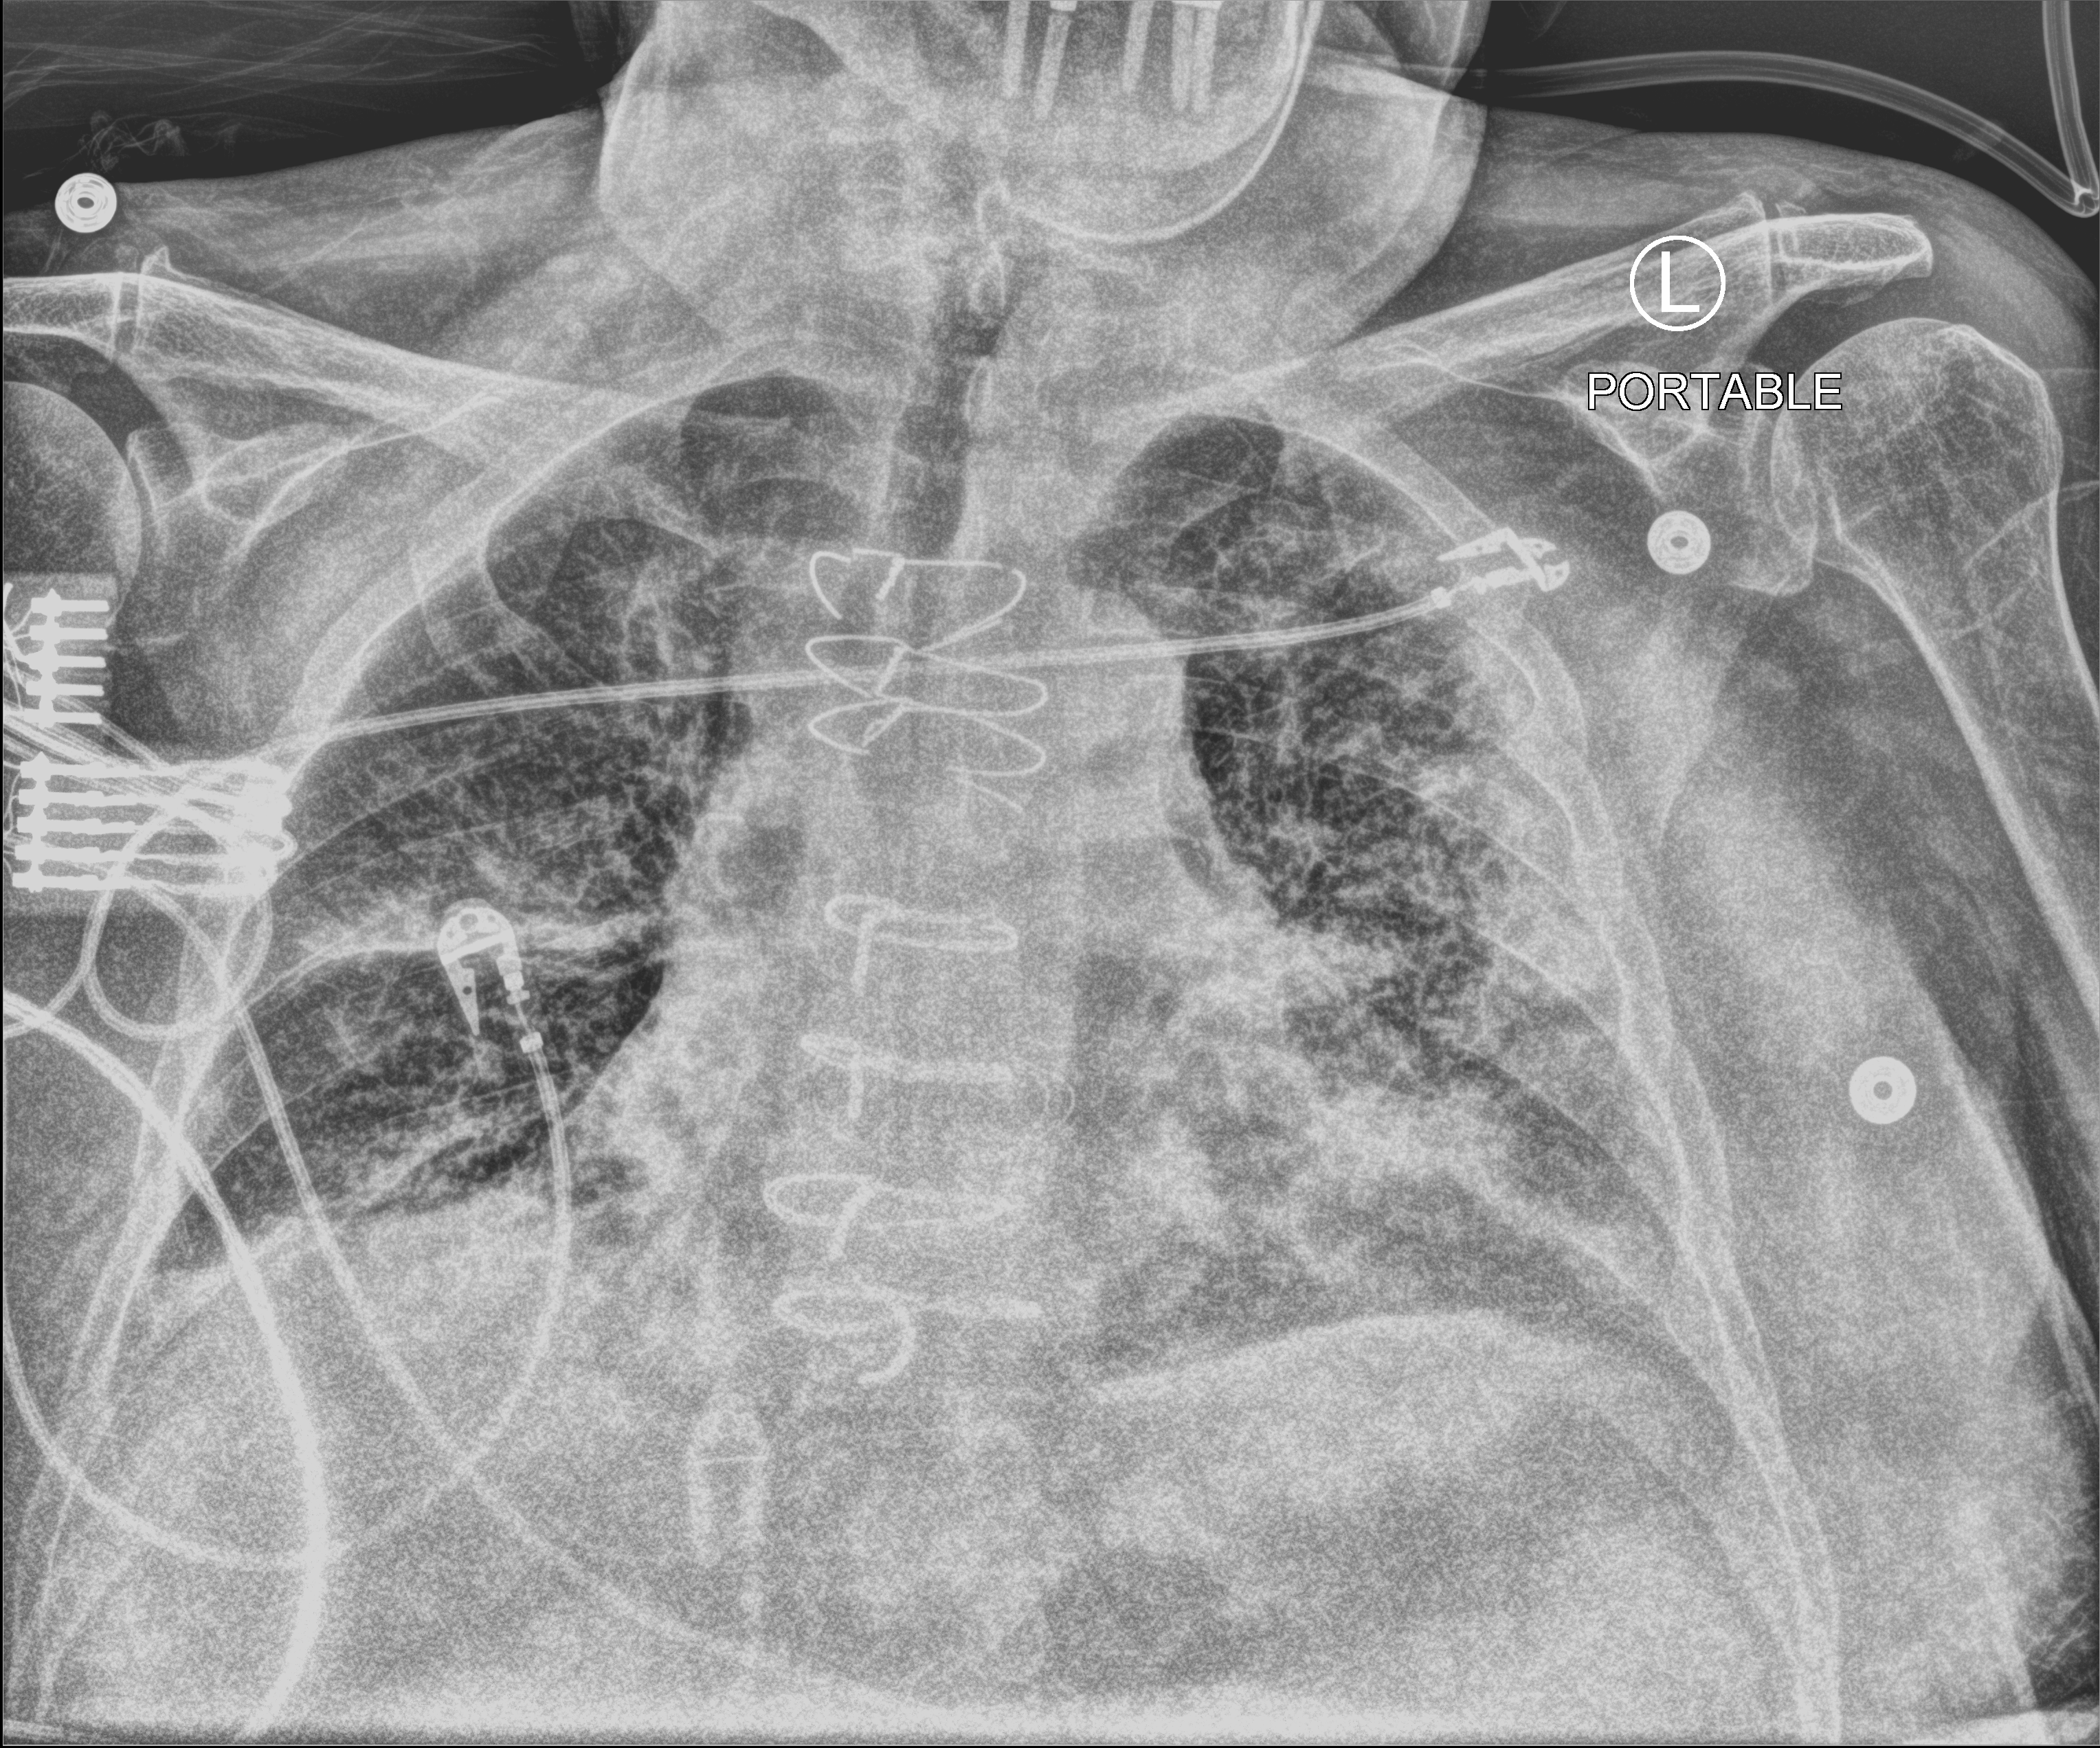
Portable chest radiograph, anteroposterior (AP) projection. Patient hospitalised with COVID-19; male, aged 75–90 years.
From the hospital-stay record, not from the radiograph (when in the stay this image was taken is not recorded): mechanically ventilated during this hospital stay: no; admitted to intensive care during this hospital stay: no; length of hospital stay: 23 days.